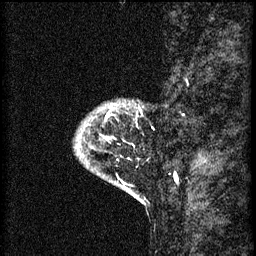
Breast MRI (dynamic contrast-enhanced), one sagittal slice. Slice 9 of 60 in the series (ordered by position). 3 images stored at this slice position (order not interpretable as contrast timing). 1.5 T. TE 4.2 ms, TR 8.2 ms. 2 mm slice thickness. 256 × 256 image matrix, field of view 180 × 180 mm. Female patient, age 41 years.
Structures marked on this image (semi-automatic segmentation, software-assisted and operator-edited):
- analysis volume of interest (the breast-tissue region the enhancement analysis was run in; not a lesion): bounding box [x1, y1, x2, y2] px = [76, 102, 141, 175]
- tumour enhancement mask (voxels above the 70 % enhancement threshold inside the analysis volume of interest): [105, 114, 108, 121]